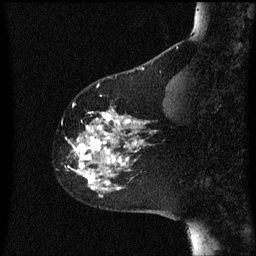
Breast MRI (dynamic contrast-enhanced), one sagittal slice; slice 17 of 60 in the series (ordered by position); dynamic contrast-enhanced series, image 2 of 3 at this slice position (ordered by acquisition); 1.5 T; TE 4.2 ms, TR 8 ms; 256 × 256 image matrix. Patient: female, 60 years.
Annotated regions visible in this slice (semi-automatic segmentation, software-assisted and operator-edited):
- analysis volume of interest (the breast-tissue region the enhancement analysis was run in; not a lesion): bounding box (x1, y1, x2, y2) in pixels: (66, 106, 158, 197)
- tumour enhancement mask (voxels above the 70 % enhancement threshold inside the analysis volume of interest): (66, 112, 147, 189)